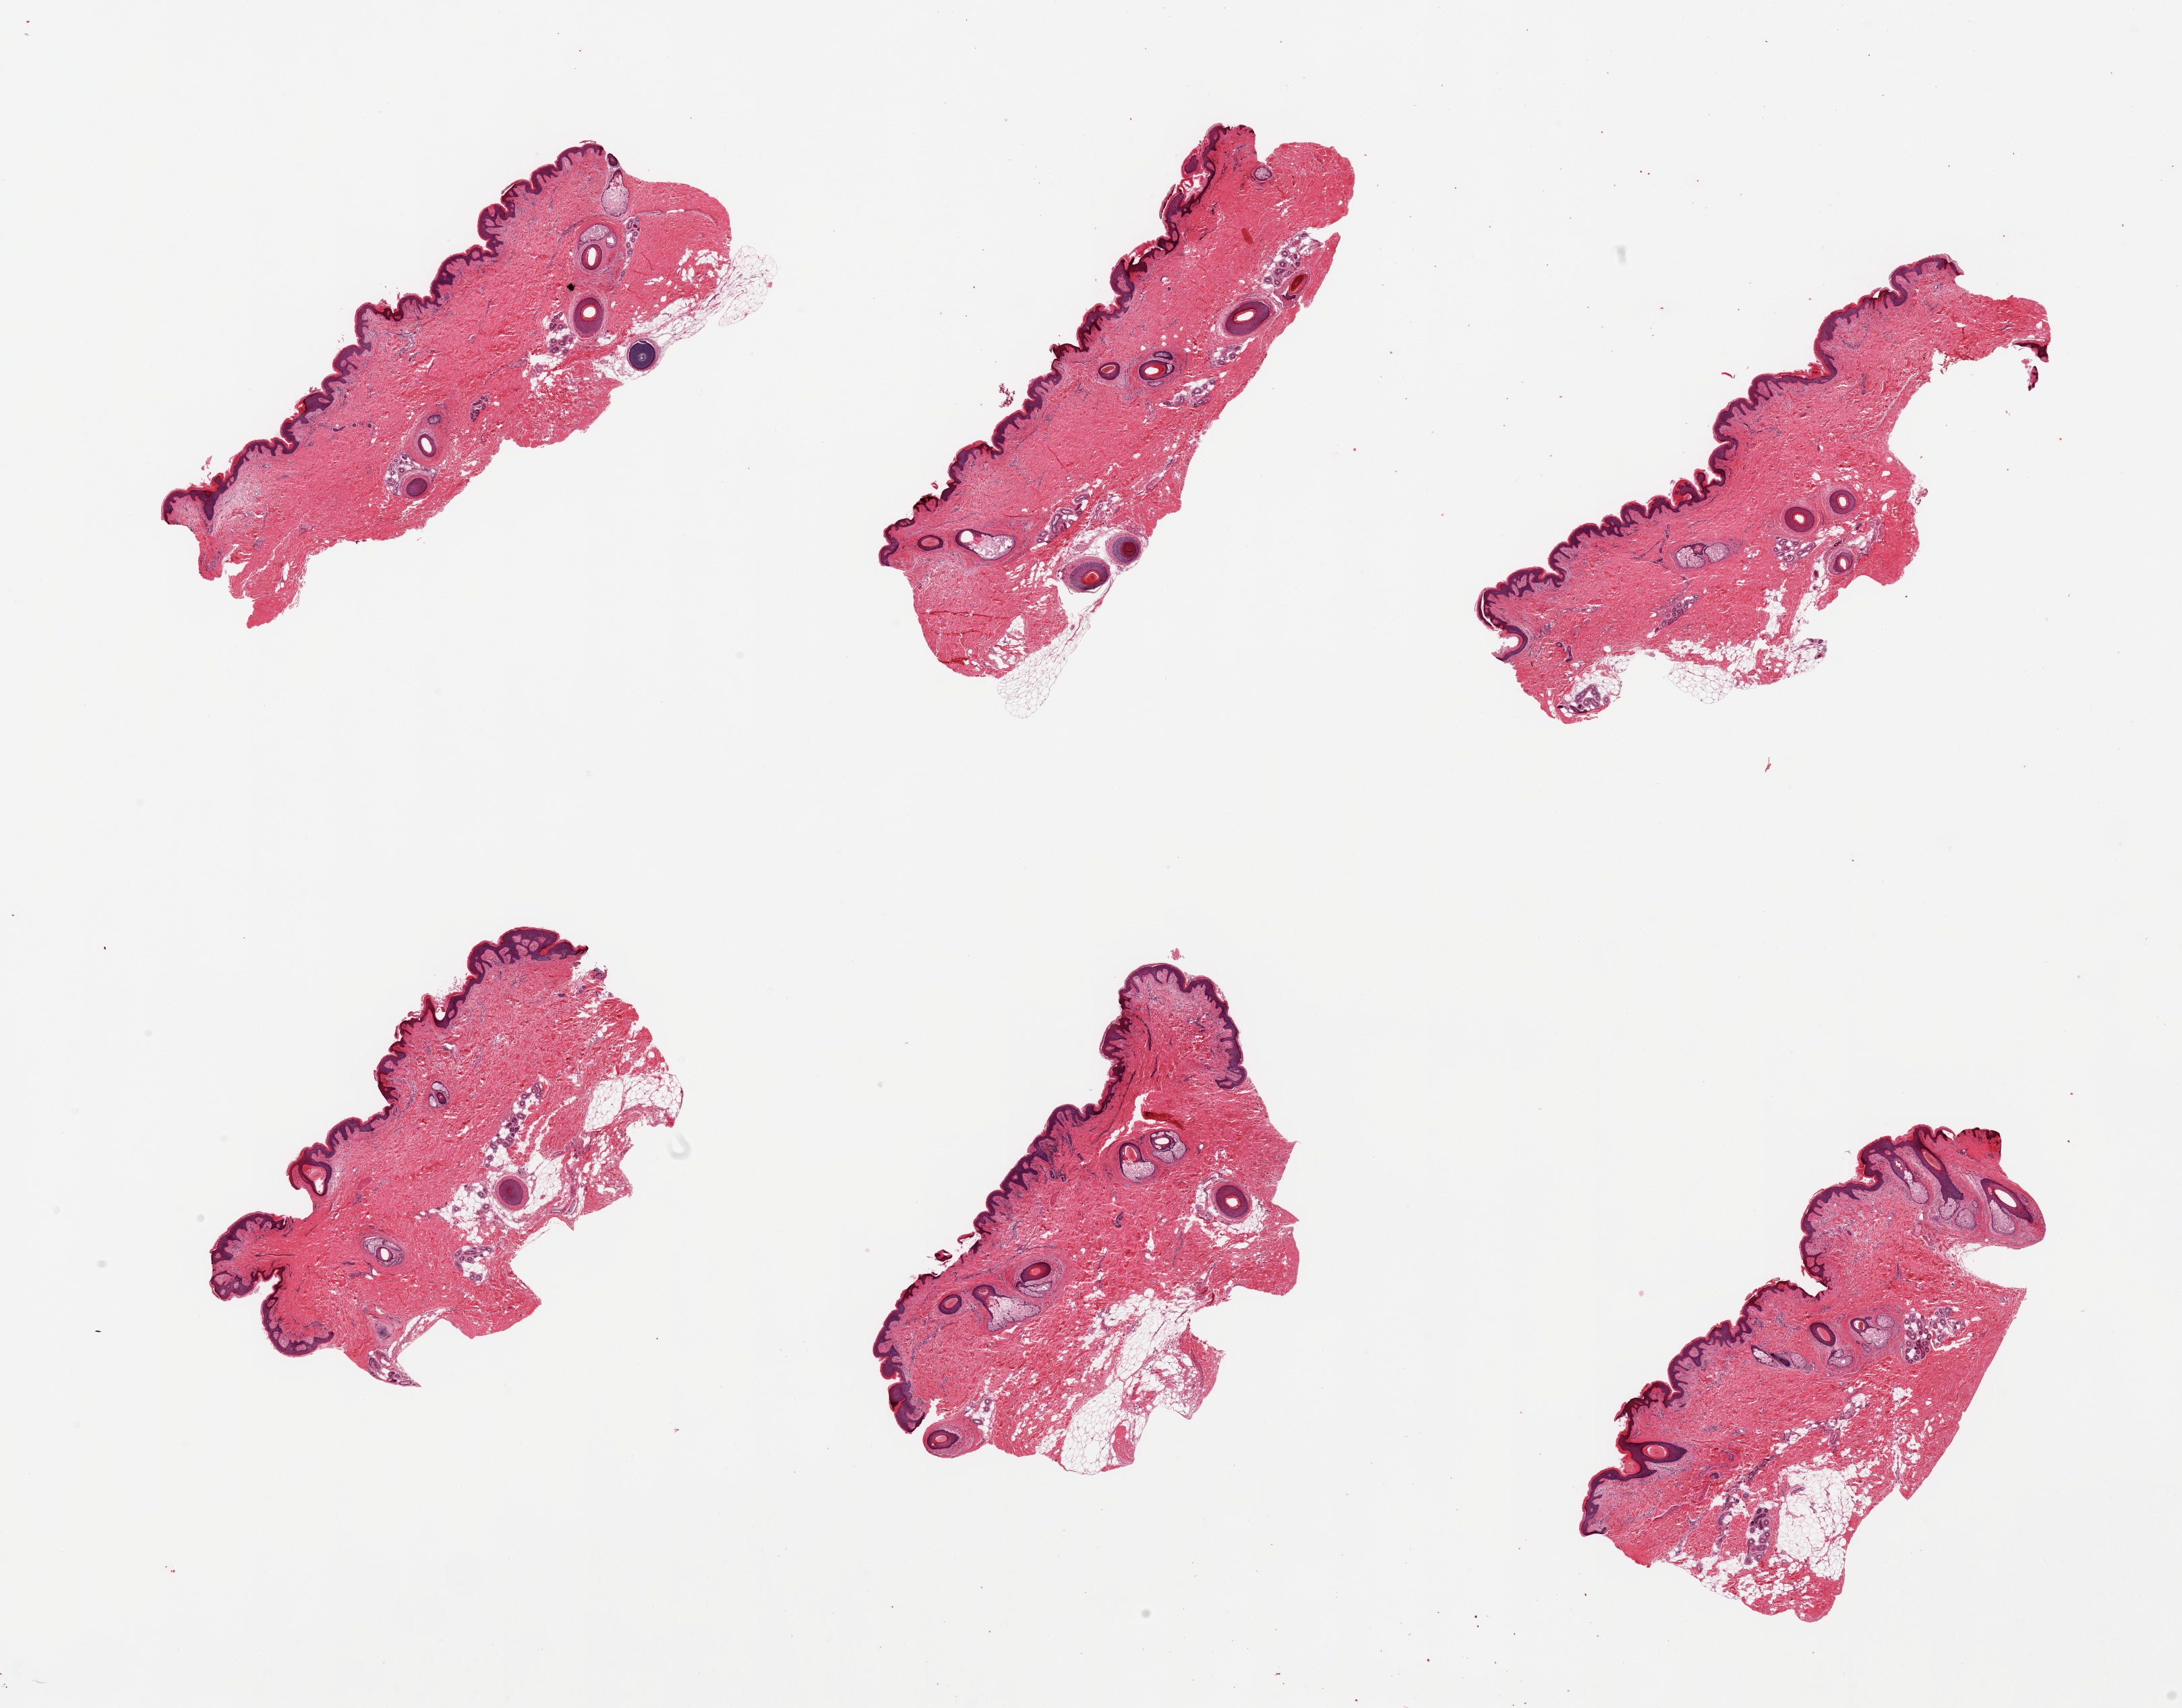
Digitized hematoxylin and eosin (H&E)-stained section, a low-resolution overview of the entire scanned area, about 25.6 x 20.0 mm (slide scanned at 20x). PAXgene-fixed, paraffin-embedded tissue. Sampled site (target tissue): skin of suprapubic region. Donor tissue sample. Donor sex: male.
* reviewer comment on this tissue sample: 6 pieces, minimal adherent dermal fat, squamous epithelium is ~70 microns